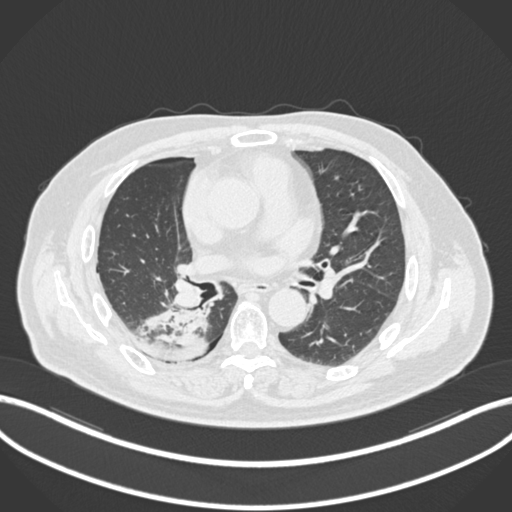
Chest CT, one axial slice; position 97 of 218 along the scan axis; reconstruction kernel B30f; lung window (W 1500 / L -600 HU); 512 × 512 image matrix, field of view 400 × 400 mm. Male patient, age 68 years. Case-level facts recorded for this patient, not image findings: clinical TNM (as recorded): T2a N0 M0.
Annotated regions visible in this slice (rectangle marked by the reading radiologist):
- lung tumour (recorded histology: adenocarcinoma): bounding box (x1, y1, x2, y2) in pixels: (132, 301, 213, 368)